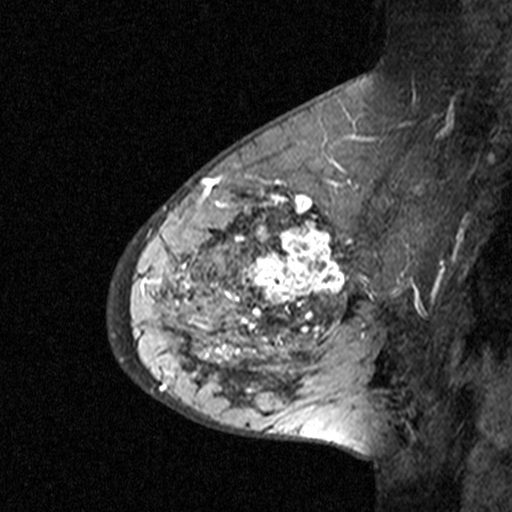
Breast MRI (dynamic contrast-enhanced), one sagittal slice; position 25 of 44 along the scan axis; dynamic contrast-enhanced study with each time point stored as its own series, time point 3 of 4 at this slice position (ordered by acquisition time); 1.5 T; TE 4.5 ms, TR 11 ms; 3 mm slice thickness; 512 × 512 image matrix. Patient: female, 65 years. From the clinical record (not read from this slice): setting: breast cancer imaged before/during neoadjuvant chemotherapy; receptor status: HER2-positive.
Annotated regions visible in this slice (semi-automatically segmented with operator editing):
- analysis volume of interest (the breast-tissue region the enhancement analysis was run in; not a lesion): bounding box (x1, y1, x2, y2) in pixels: (182, 190, 353, 361)
- tumour enhancement mask (voxels above the 90 % enhancement threshold inside the analysis volume of interest): (205, 190, 351, 358)